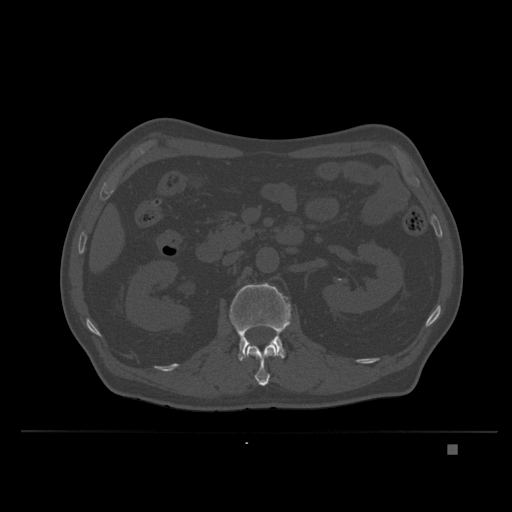
CT including the spine, one axial slice. Position 126 of 435 along the scan axis. Bone window (W 1800 / L 400 HU). 1.5 mm slice thickness. 512 × 512 image matrix. Patient: male, 73 years. Case-level facts recorded for this patient, not image findings: primary cancer: skin.
Annotated regions visible in this slice (semi-automatic segmentation, software-assisted and operator-edited):
- L1 vertebra: bounding box [x1, y1, x2, y2] px = [243, 340, 278, 386]
- L2 vertebra: [229, 282, 292, 361]